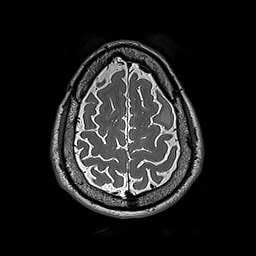
Brain MRI from a brain-tumour surgery series, one axial slice; slice 56 of 192 in the series (ordered by position); 1 mm slice thickness; 256 × 256 image matrix, field of view 250 × 250 mm. Case-level facts recorded for this patient, not image findings: histopathology: Astrocytoma; WHO grade: 2; IDH mutation: yes; tumour location: Left Frontal.
Outlined on this slice (outlined manually by an expert reader):
- tumour: bounding box <158,108,170,127> (left, top, right, bottom; pixels)